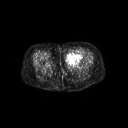
FDG PET of an extremity soft-tissue mass (from a PET/CT study), one axial slice. Position 25 of 267 along the scan axis. 3.27 mm slice thickness. 128 × 128 image matrix. Female patient, age 47 years. From the clinical record (not read from this slice): histological type: myxofibrosarcoma; grade: intermediate; site of the primary tumour: left thigh.
Outlined on this slice (expert contour drawn on MRI and transferred to this co-registered scan by the dataset authors):
- gross tumour volume including surrounding oedema: box from (x=65, y=51) to (x=82, y=64) px
- gross tumour volume (mass): (x=66, y=51)–(x=82, y=64)